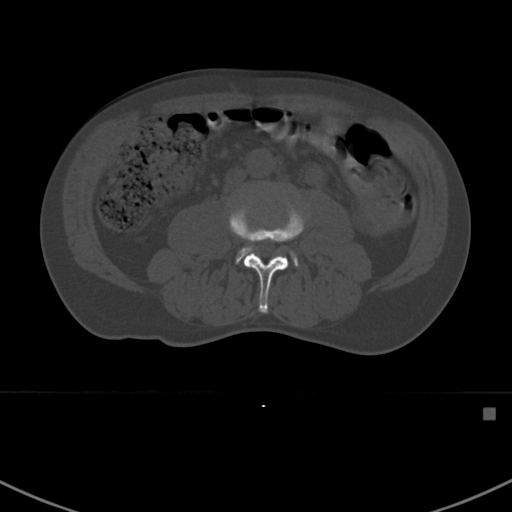
CT including the spine, one axial slice; position 257 of 412 along the scan axis; 120 kVp; bone window (W 1800 / L 400 HU); 512 × 512 image matrix, field of view 358 × 358 mm. Male patient, age 59 years. From the clinical record (not read from this slice): primary cancer: prostate.
Outlined on this slice (semi-automatically segmented with operator editing):
- L3 vertebra: bounding box (x1, y1, x2, y2) in pixels: (229, 201, 305, 313)
- L4 vertebra: (235, 245, 298, 266)